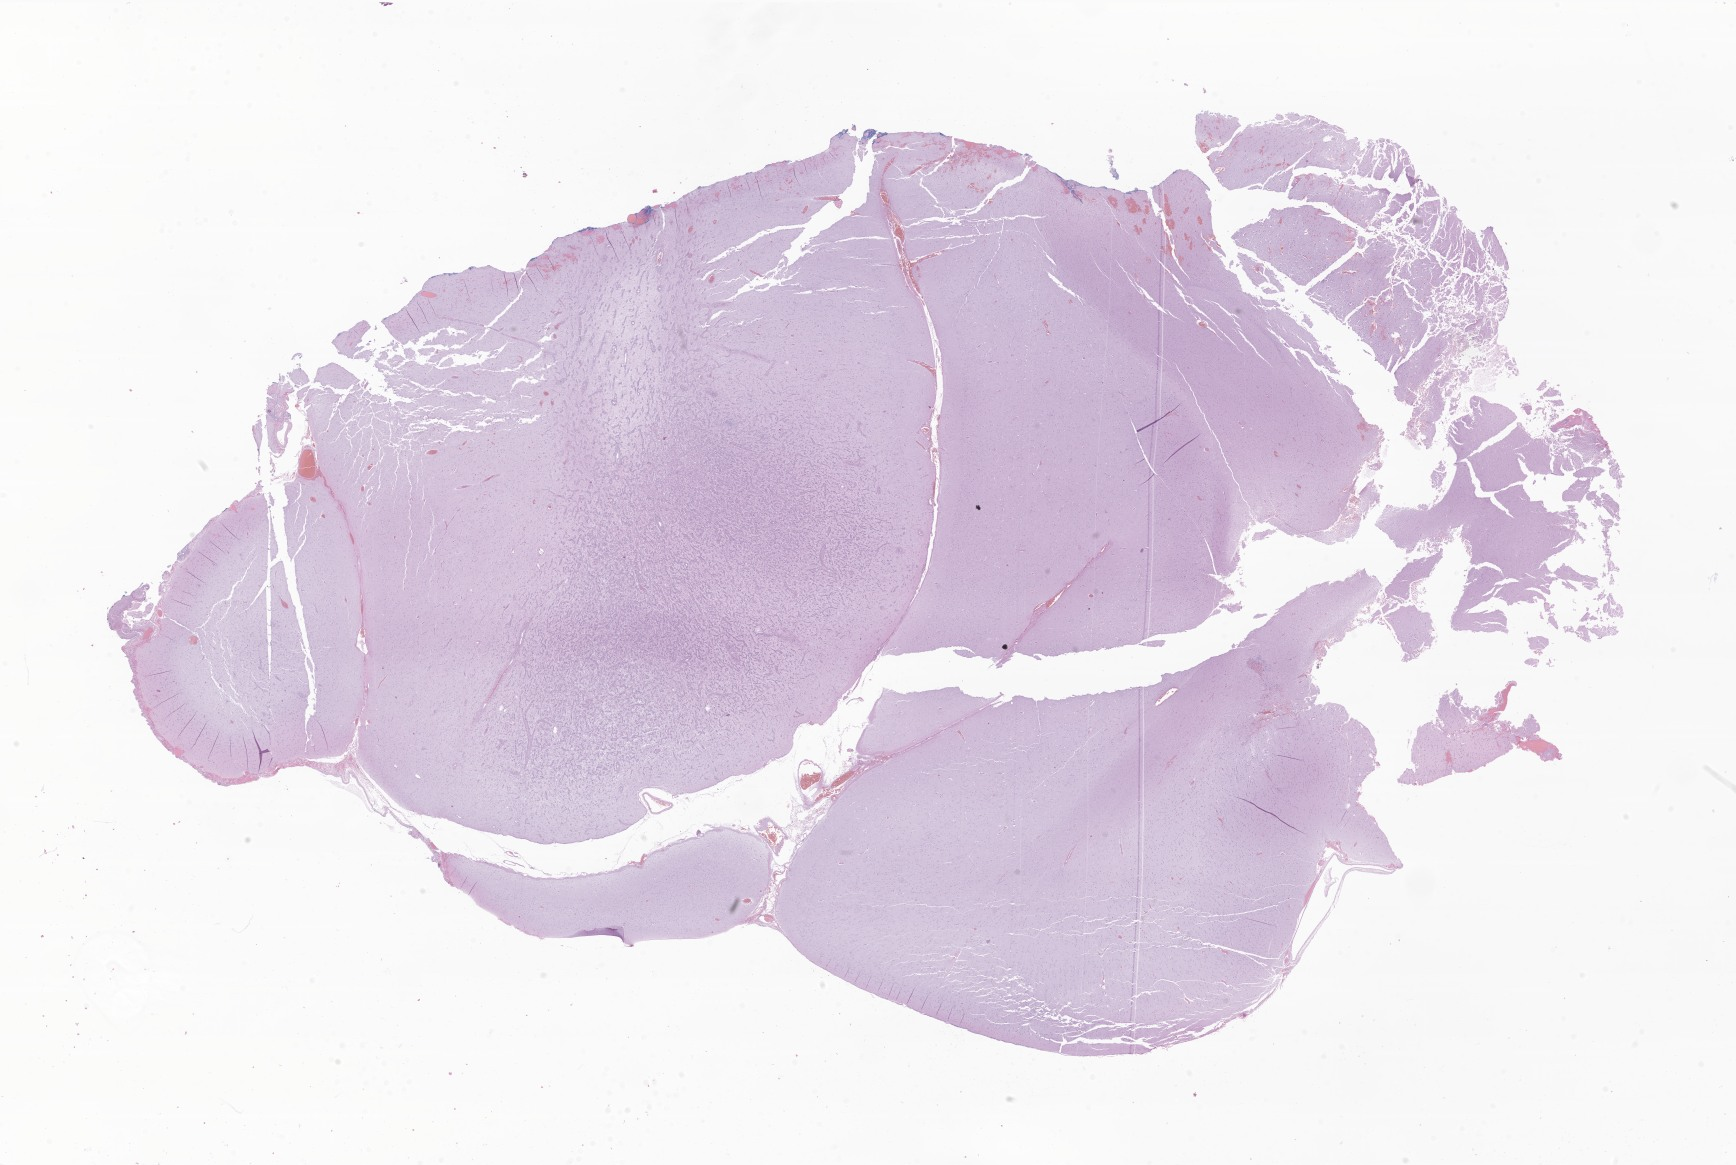
Digitized H&E-stained section of tumor tissue from the brain, low-resolution overview of the scanned area, about 29.3 x 19.6 mm. Formalin-fixed, paraffin-embedded (FFPE) tissue. Patient: male, age 72 months (6 years).
* diagnosis: Angiocentric immunoproliferative lesion